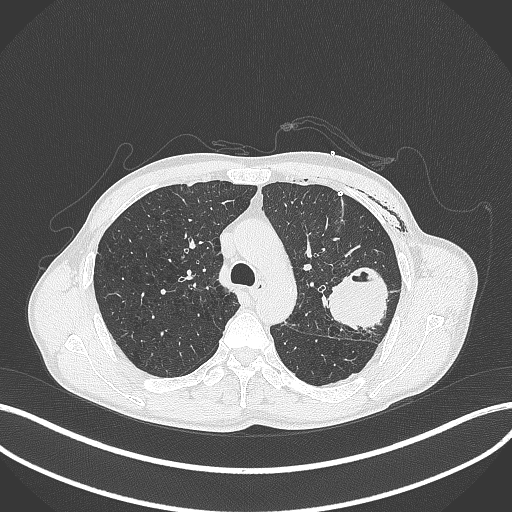
Chest CT, one axial slice. Position 283 of 457 along the scan axis. Reconstruction kernel B70f. Lung window (W 1500 / L -600 HU). 1 mm slice thickness. 512 × 512 image matrix, field of view 400 × 400 mm. Patient: male, 58 years. From the clinical record (not read from this slice): clinical TNM (as recorded): T3 N0 M0.
Annotated regions visible in this slice (rectangle marked by the reading radiologist):
- lung tumour (recorded histology: adenocarcinoma): box from (x=323, y=265) to (x=390, y=336) px